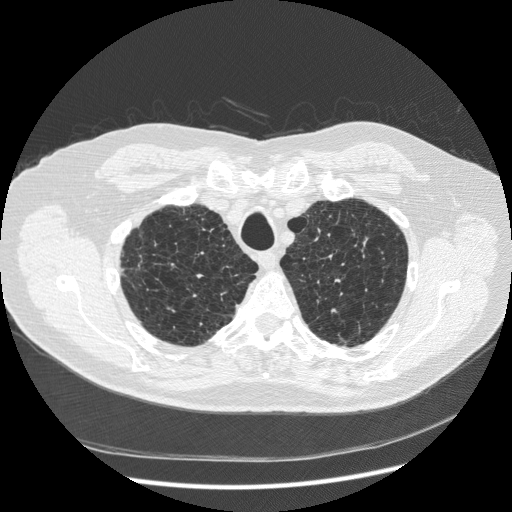
Axial slice from a low-dose chest CT screening exam, baseline screening round, lung window (W 1500 / L -600 HU), 1.25 mm slice thickness, standard (soft-tissue) reconstruction kernel (STANDARD), slice 47 of 265 in the series. Male participant, aged 70 years at enrolment.
- Expert-annotated lung lesion, bounding box <330,215,385,270> (left, top, right, bottom; pixels).
- The screening reader recorded 2 non-calcified nodules or masses ≥4 mm on this exam (right lower lobe, right lower lobe); which of them this box marks is not recorded.
- Official screen result: positive, change unspecified: nodule(s) >= 4 mm or enlarging nodule(s), mass(es), or other non-specific abnormalities suspicious for lung cancer.
- Lung cancer was diagnosed 816 days after this screen (after the third annual screen): squamous cell carcinoma, NOS, left upper lobe, moderately differentiated (G2), stage IA (AJCC 6th edition), 18 mm at pathology.